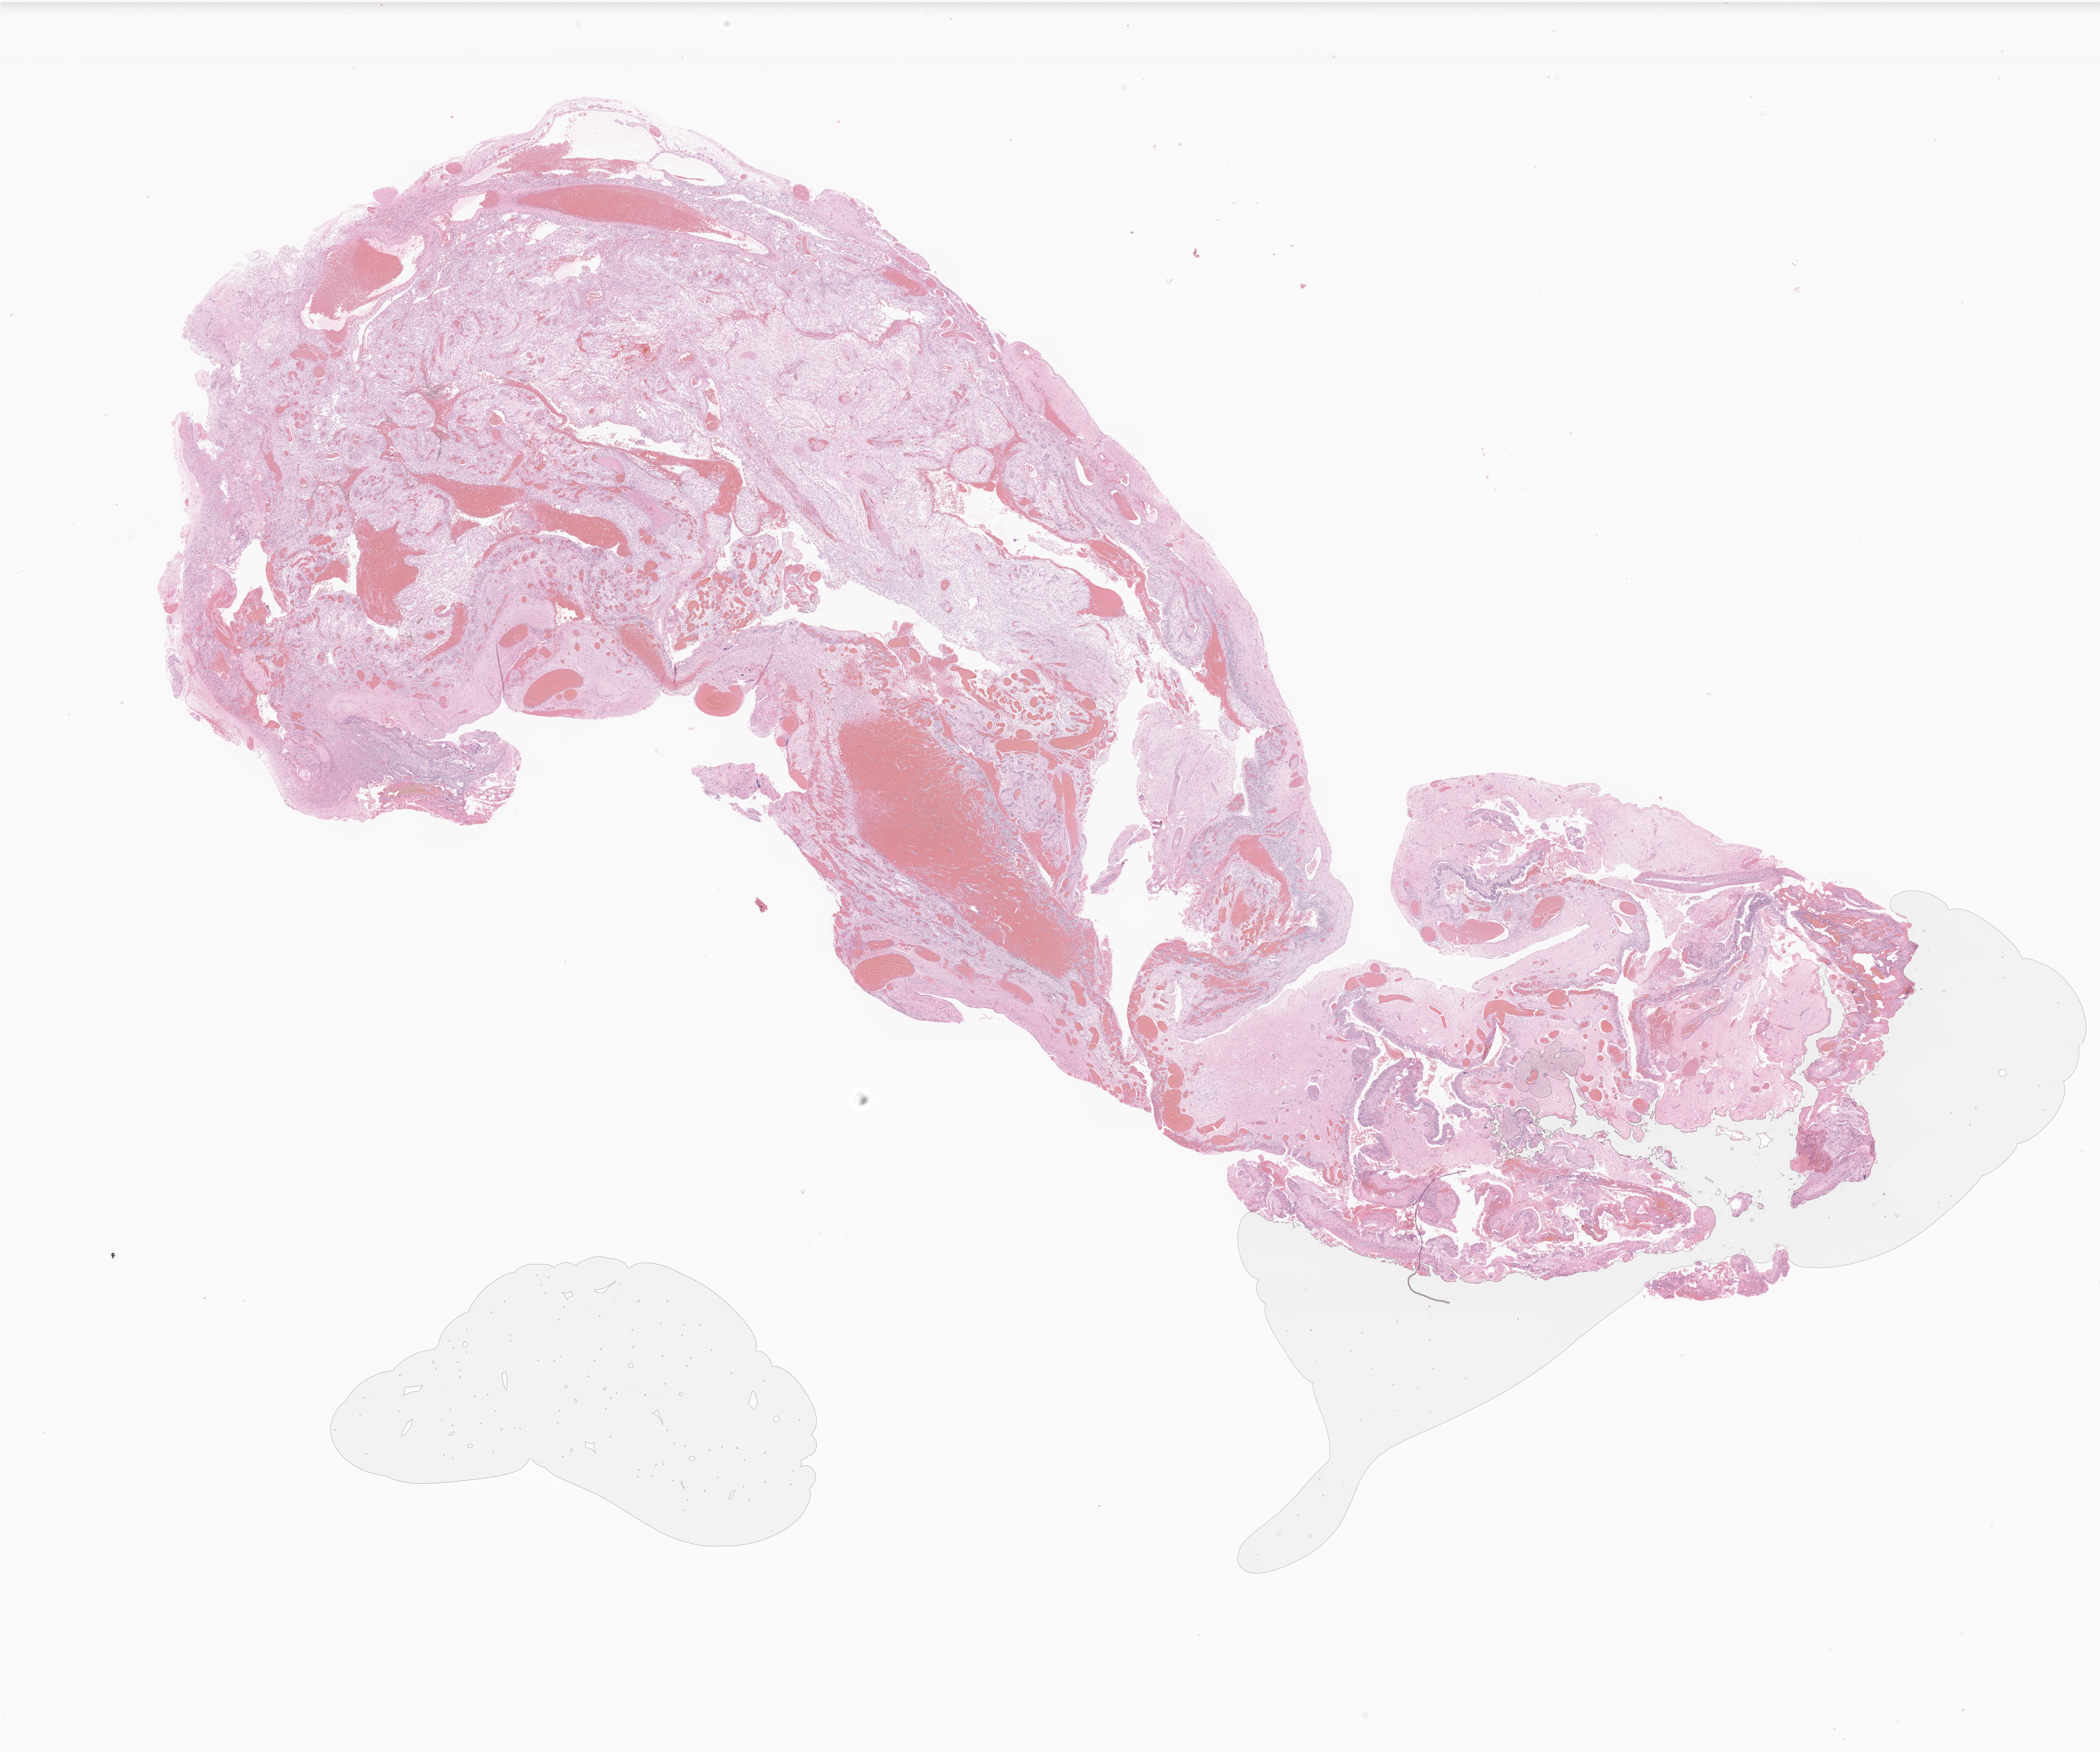
Digitized hematoxylin and eosin (H&E)-stained section of tumor tissue from the brain — low-resolution overview of the scanned area, about 25.3 x 21.1 mm; formalin-fixed paraffin-embedded section. Patient: female, age 87 months (7 years 3 months).
• diagnosis (ICD-O-3 morphology term): Pilocytic astrocytoma